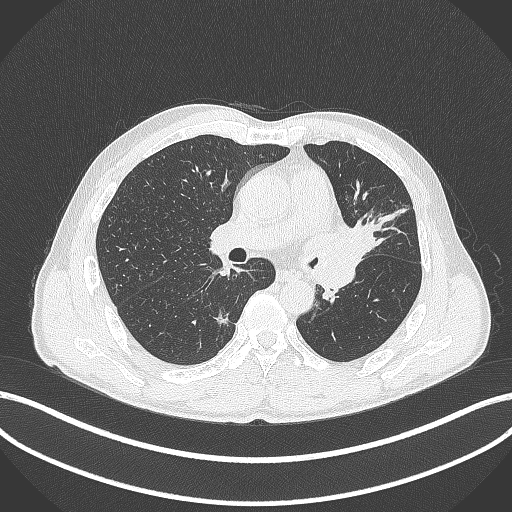
Chest CT, one axial slice; position 238 of 429 along the scan axis; reconstruction kernel B70f; lung window (W 1500 / L -600 HU); 512 × 512 image matrix, field of view 400 × 400 mm. Patient: male, 57 years. Case-level facts recorded for this patient, not image findings: clinical TNM (as recorded): T2b N0 M0.
Annotated regions visible in this slice (rectangle marked by the reading radiologist):
- lung tumour (recorded histology: squamous cell carcinoma): bounding box [x1, y1, x2, y2] px = [327, 217, 378, 265]